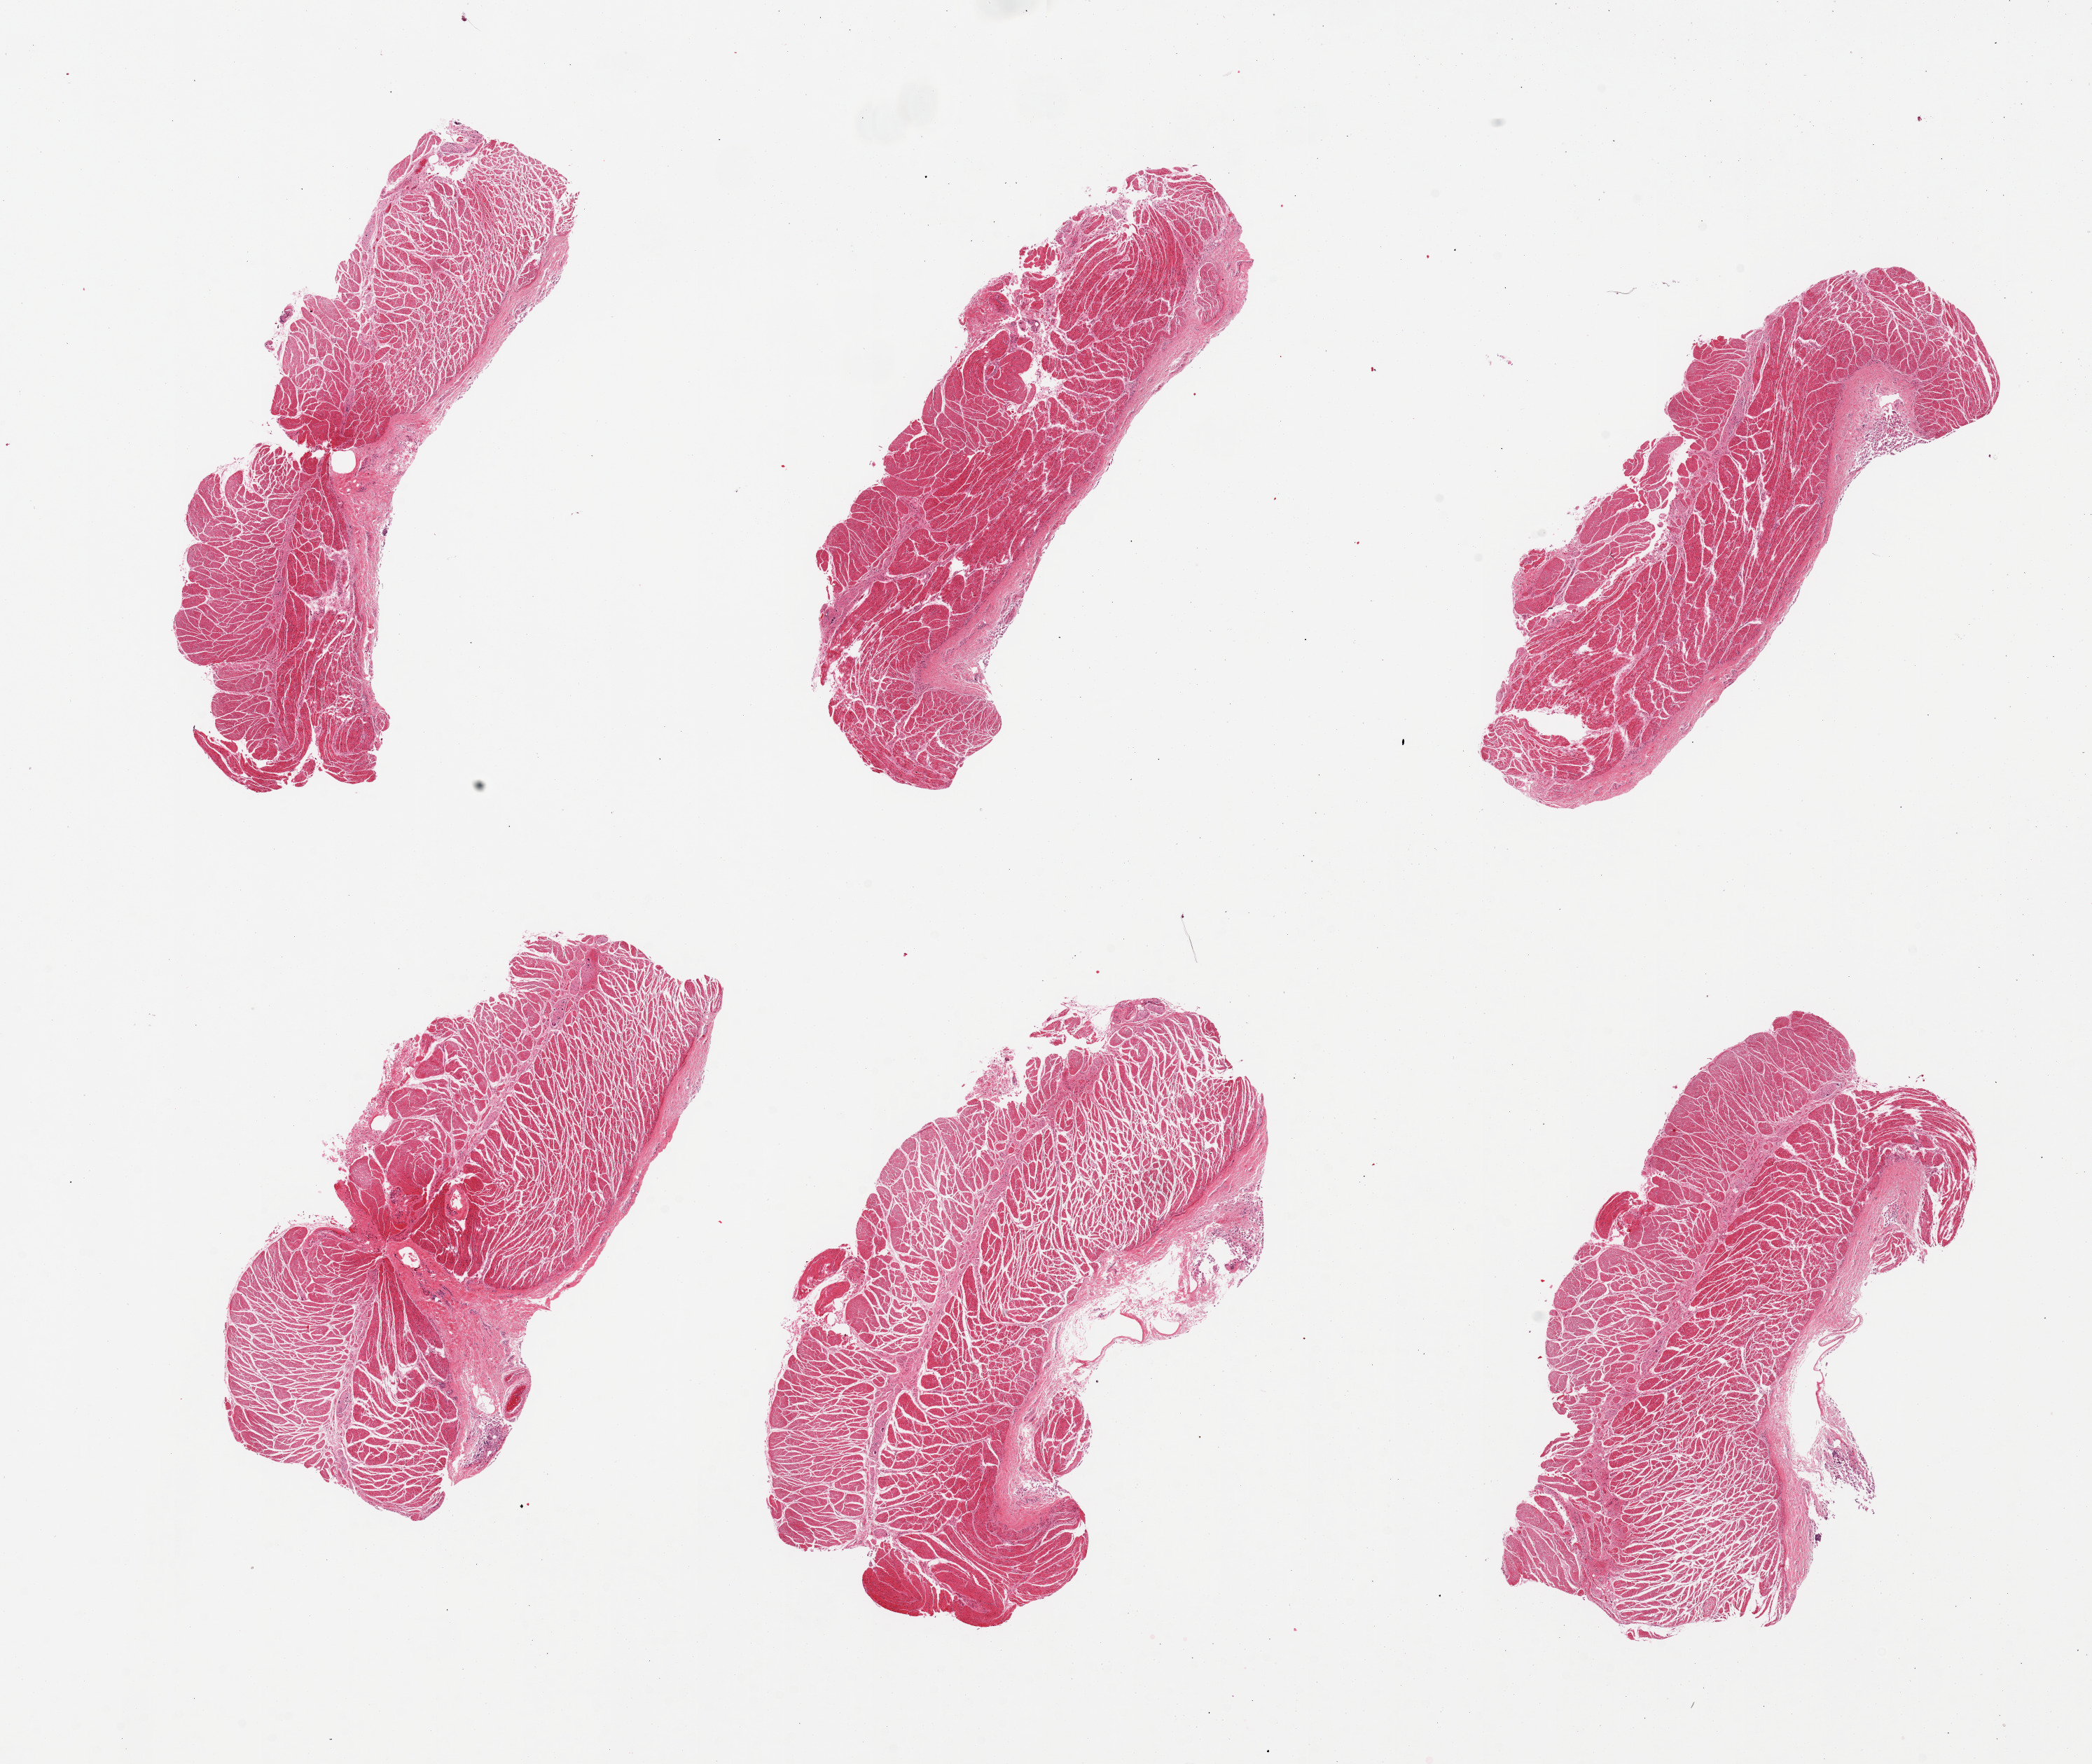
Whole-slide image, haematoxylin and eosin stain, a low-resolution overview of the entire scanned area, about 23.6 x 19.9 mm (acquisition: 20x scan). PAXgene-fixed paraffin-embedded (PFPE) section. Target tissue: esophageal muscle. Donor tissue sample. Male donor.
Pathologist's review note for this sample: 6 pieces, well trimmed, focal detached fragmented squamous epithelium.